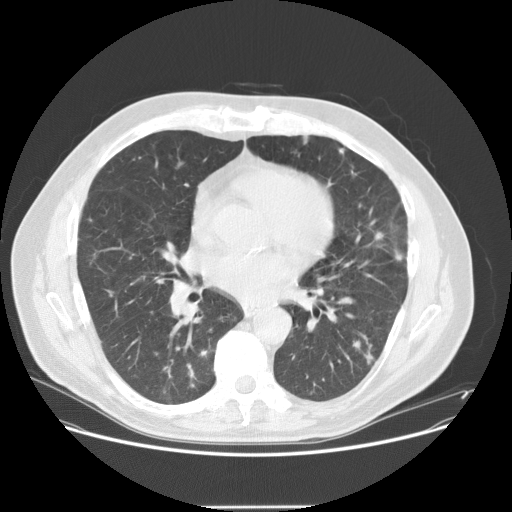
Low-dose screening chest CT, one axial slice; slice 71 of 143 in the series (ordered by position); reconstruction kernel STANDARD; 120 kVp; lung window (W 1500 / L -600 HU); 2.5 mm slice thickness; 512 × 512 image matrix, field of view 400 × 400 mm.
Annotated regions visible in this slice (manually delineated by an expert):
- lesion 7 (tumor): box from (x=364, y=351) to (x=374, y=364) px